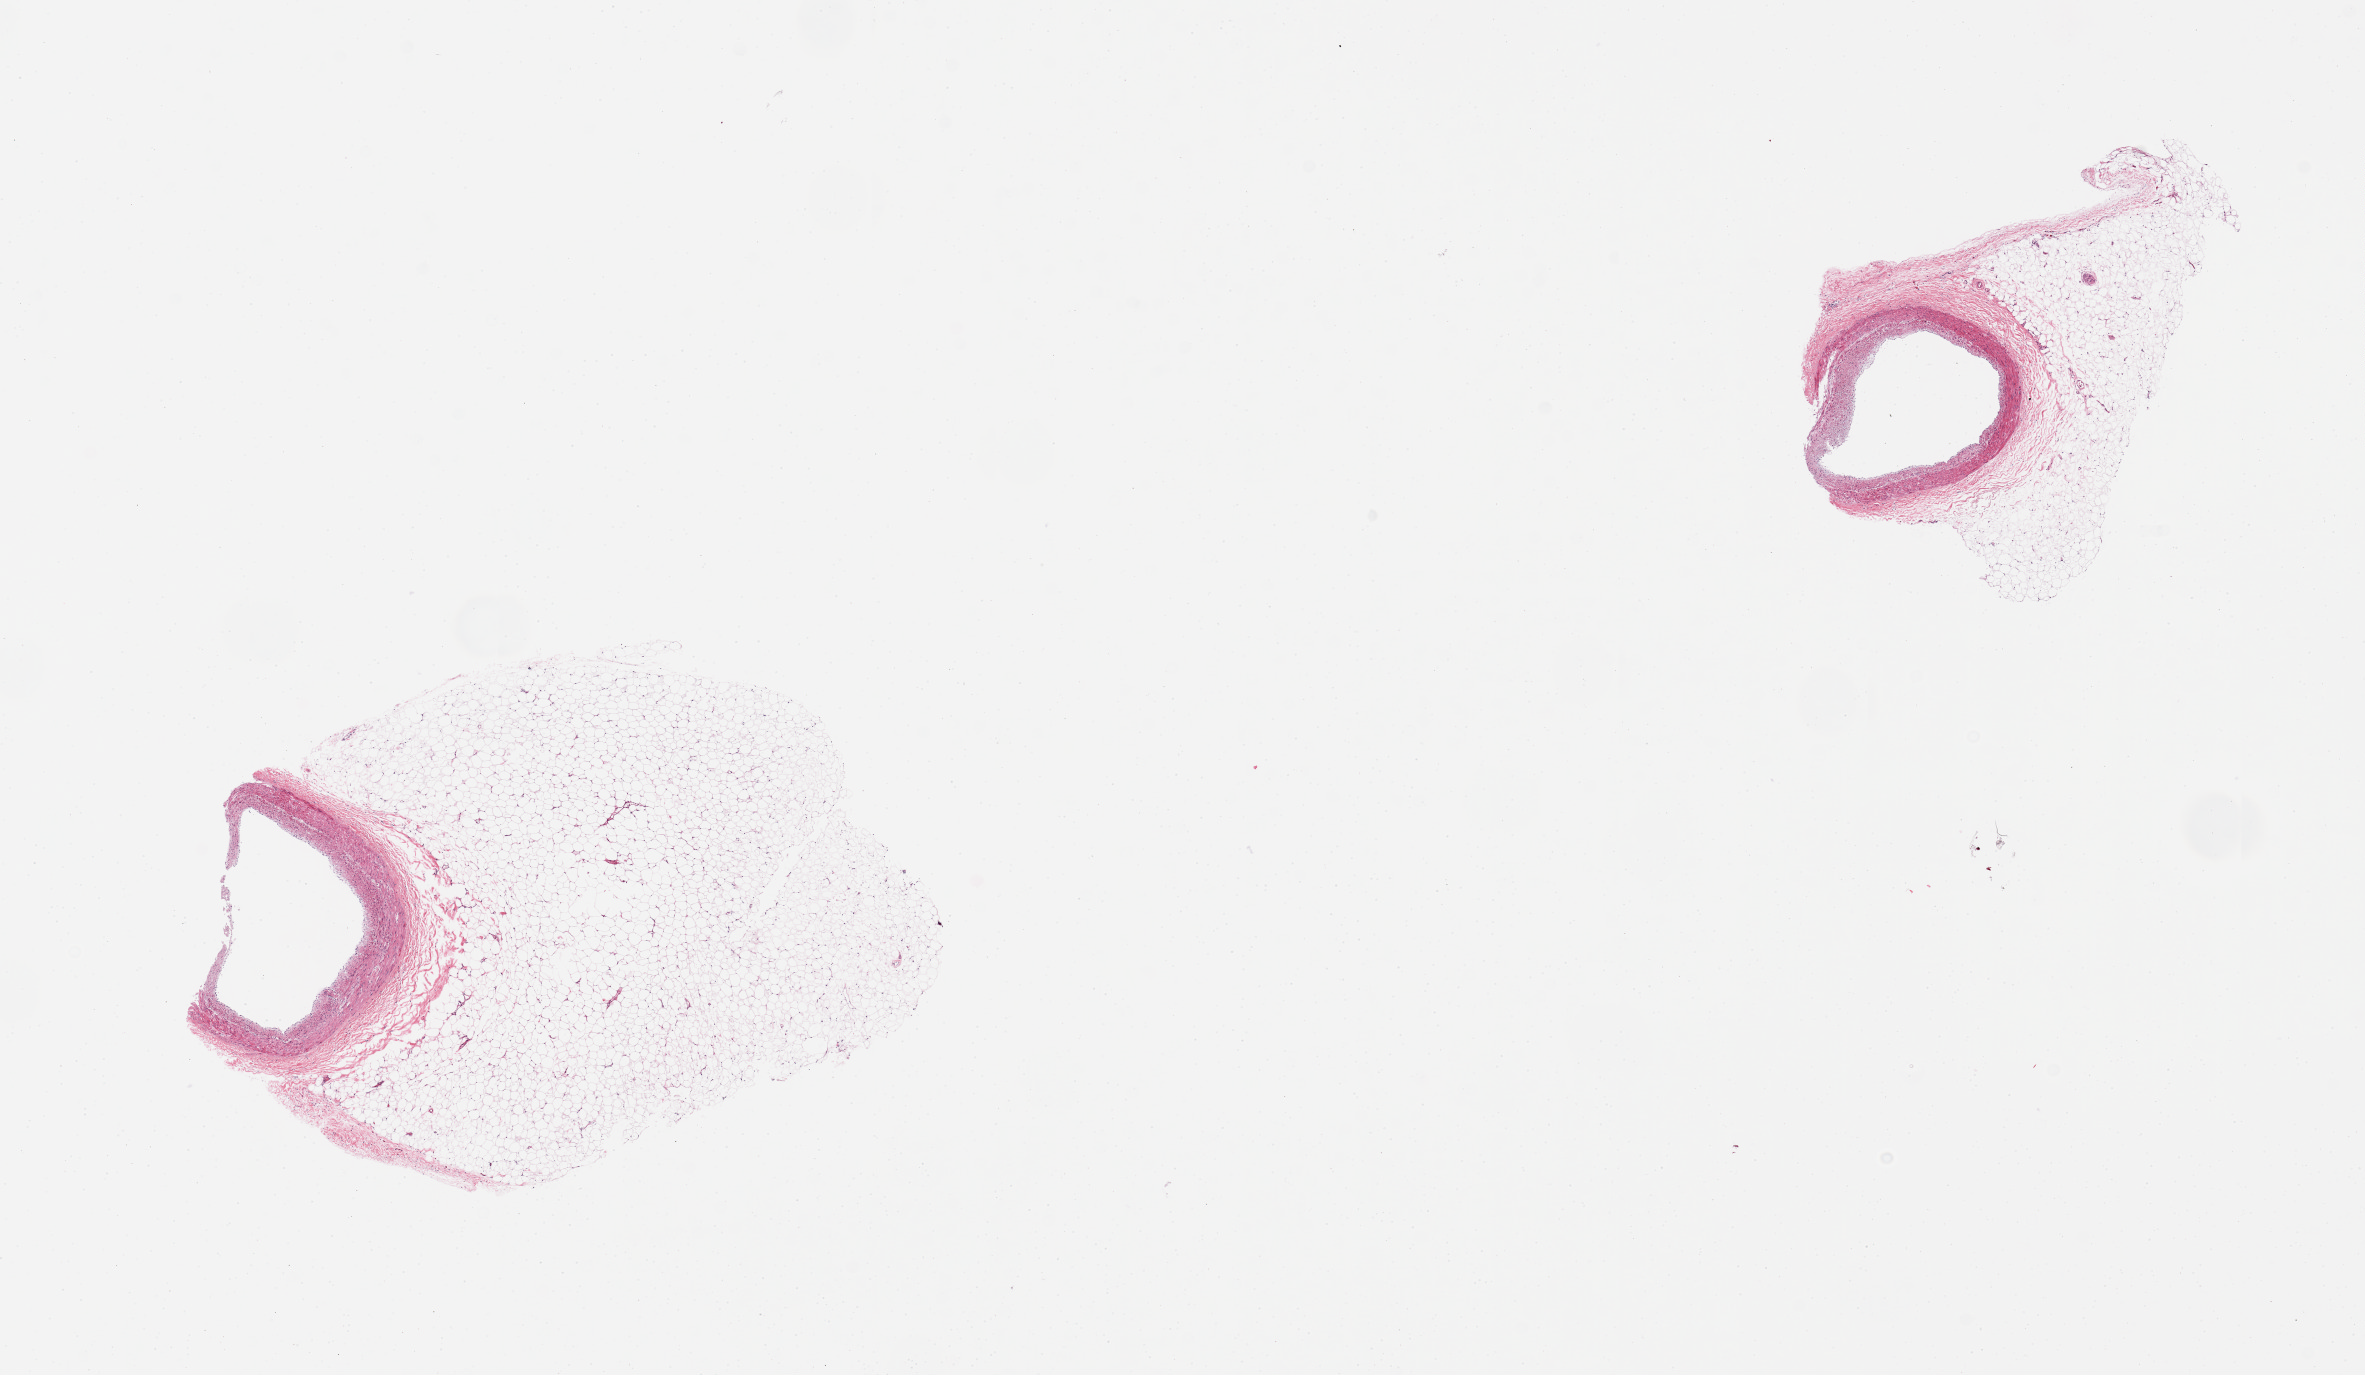
Whole-slide image, hematoxylin and eosin (H&E) stain — shown as a low-resolution overview of the whole scanned area (about 18.7 x 10.9 mm). PAXgene-fixed, paraffin-embedded tissue. Sampled site (target tissue): coronary artery. Donor tissue sample. Female donor.
- pathologist's review note for this sample: 2 pieces, both with significant attached fat up to 3.8mm, artery represents only 10% and 40% of tissue due to included adipose tissue